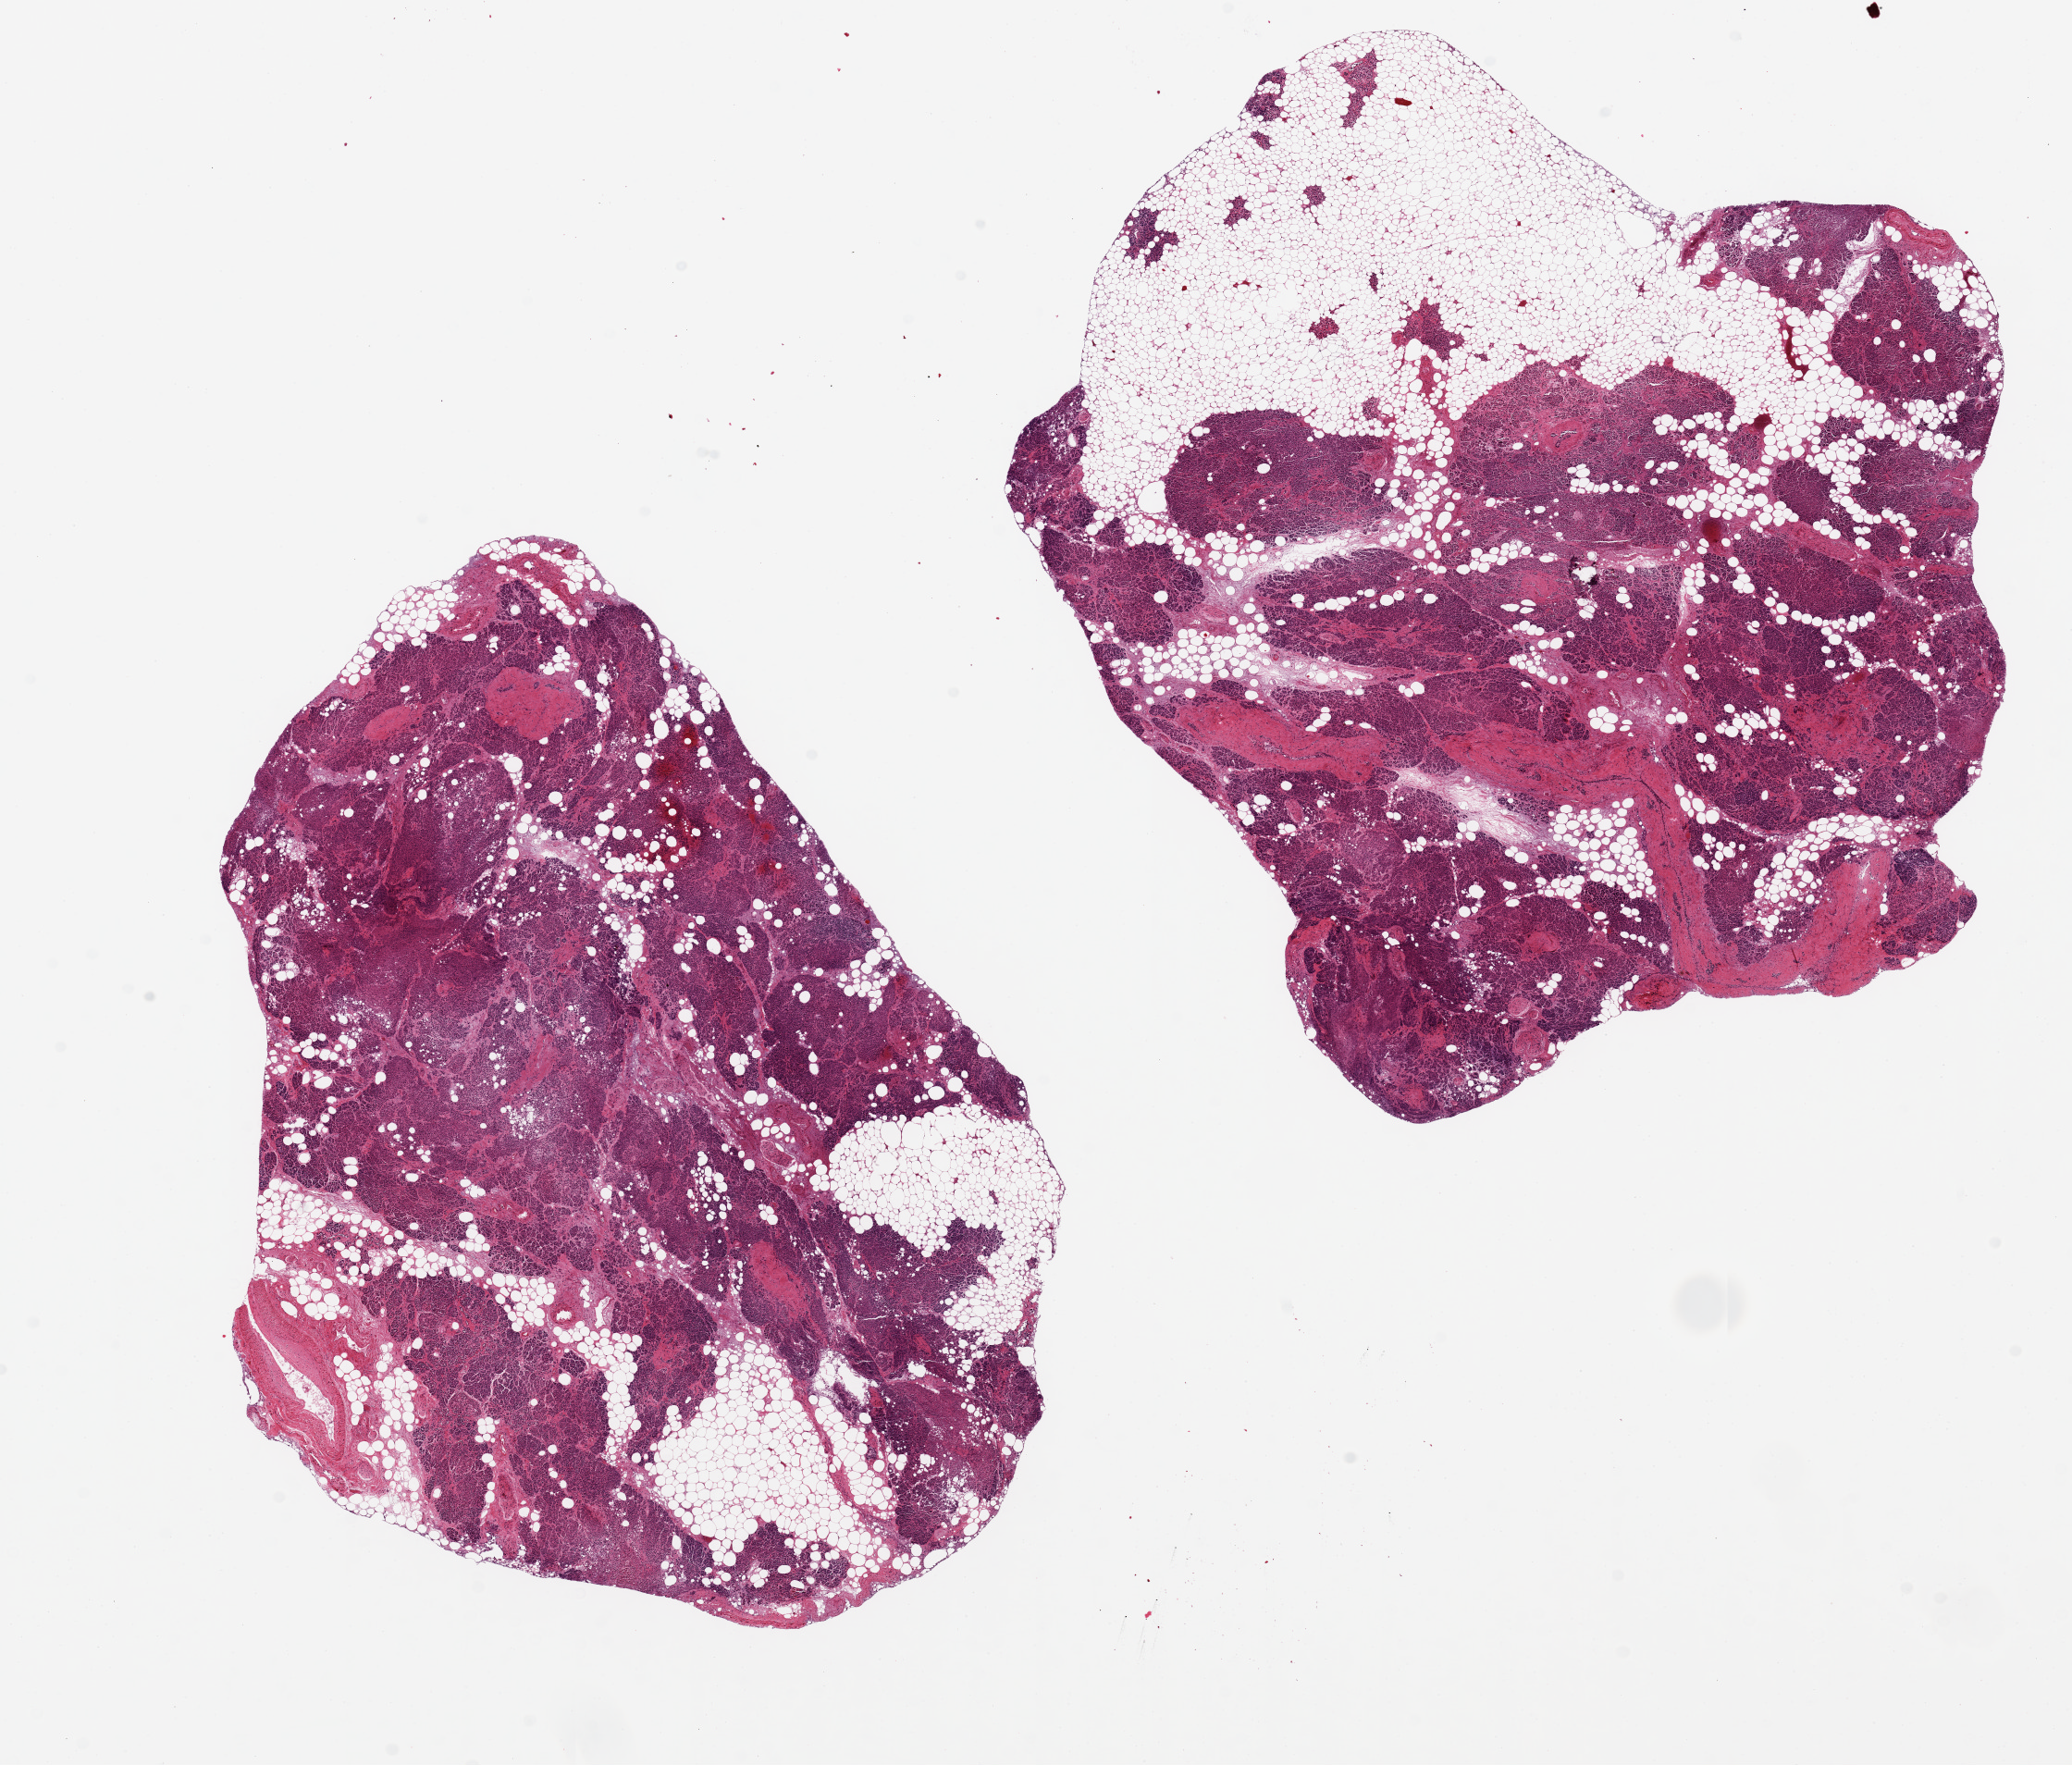
Digitized hematoxylin and eosin (H&E)-stained section, whole scanned area (about 17.7 x 15.1 mm, from a 20x scan) shown as a low-resolution overview; PAXgene-fixed paraffin-embedded (PFPE) section; target tissue: pancreas; tissue donor sample. Donor sex: male.
Review note (as recorded): 2 aliquots, ~9x7mm, ~20% fat, saponificaiton.